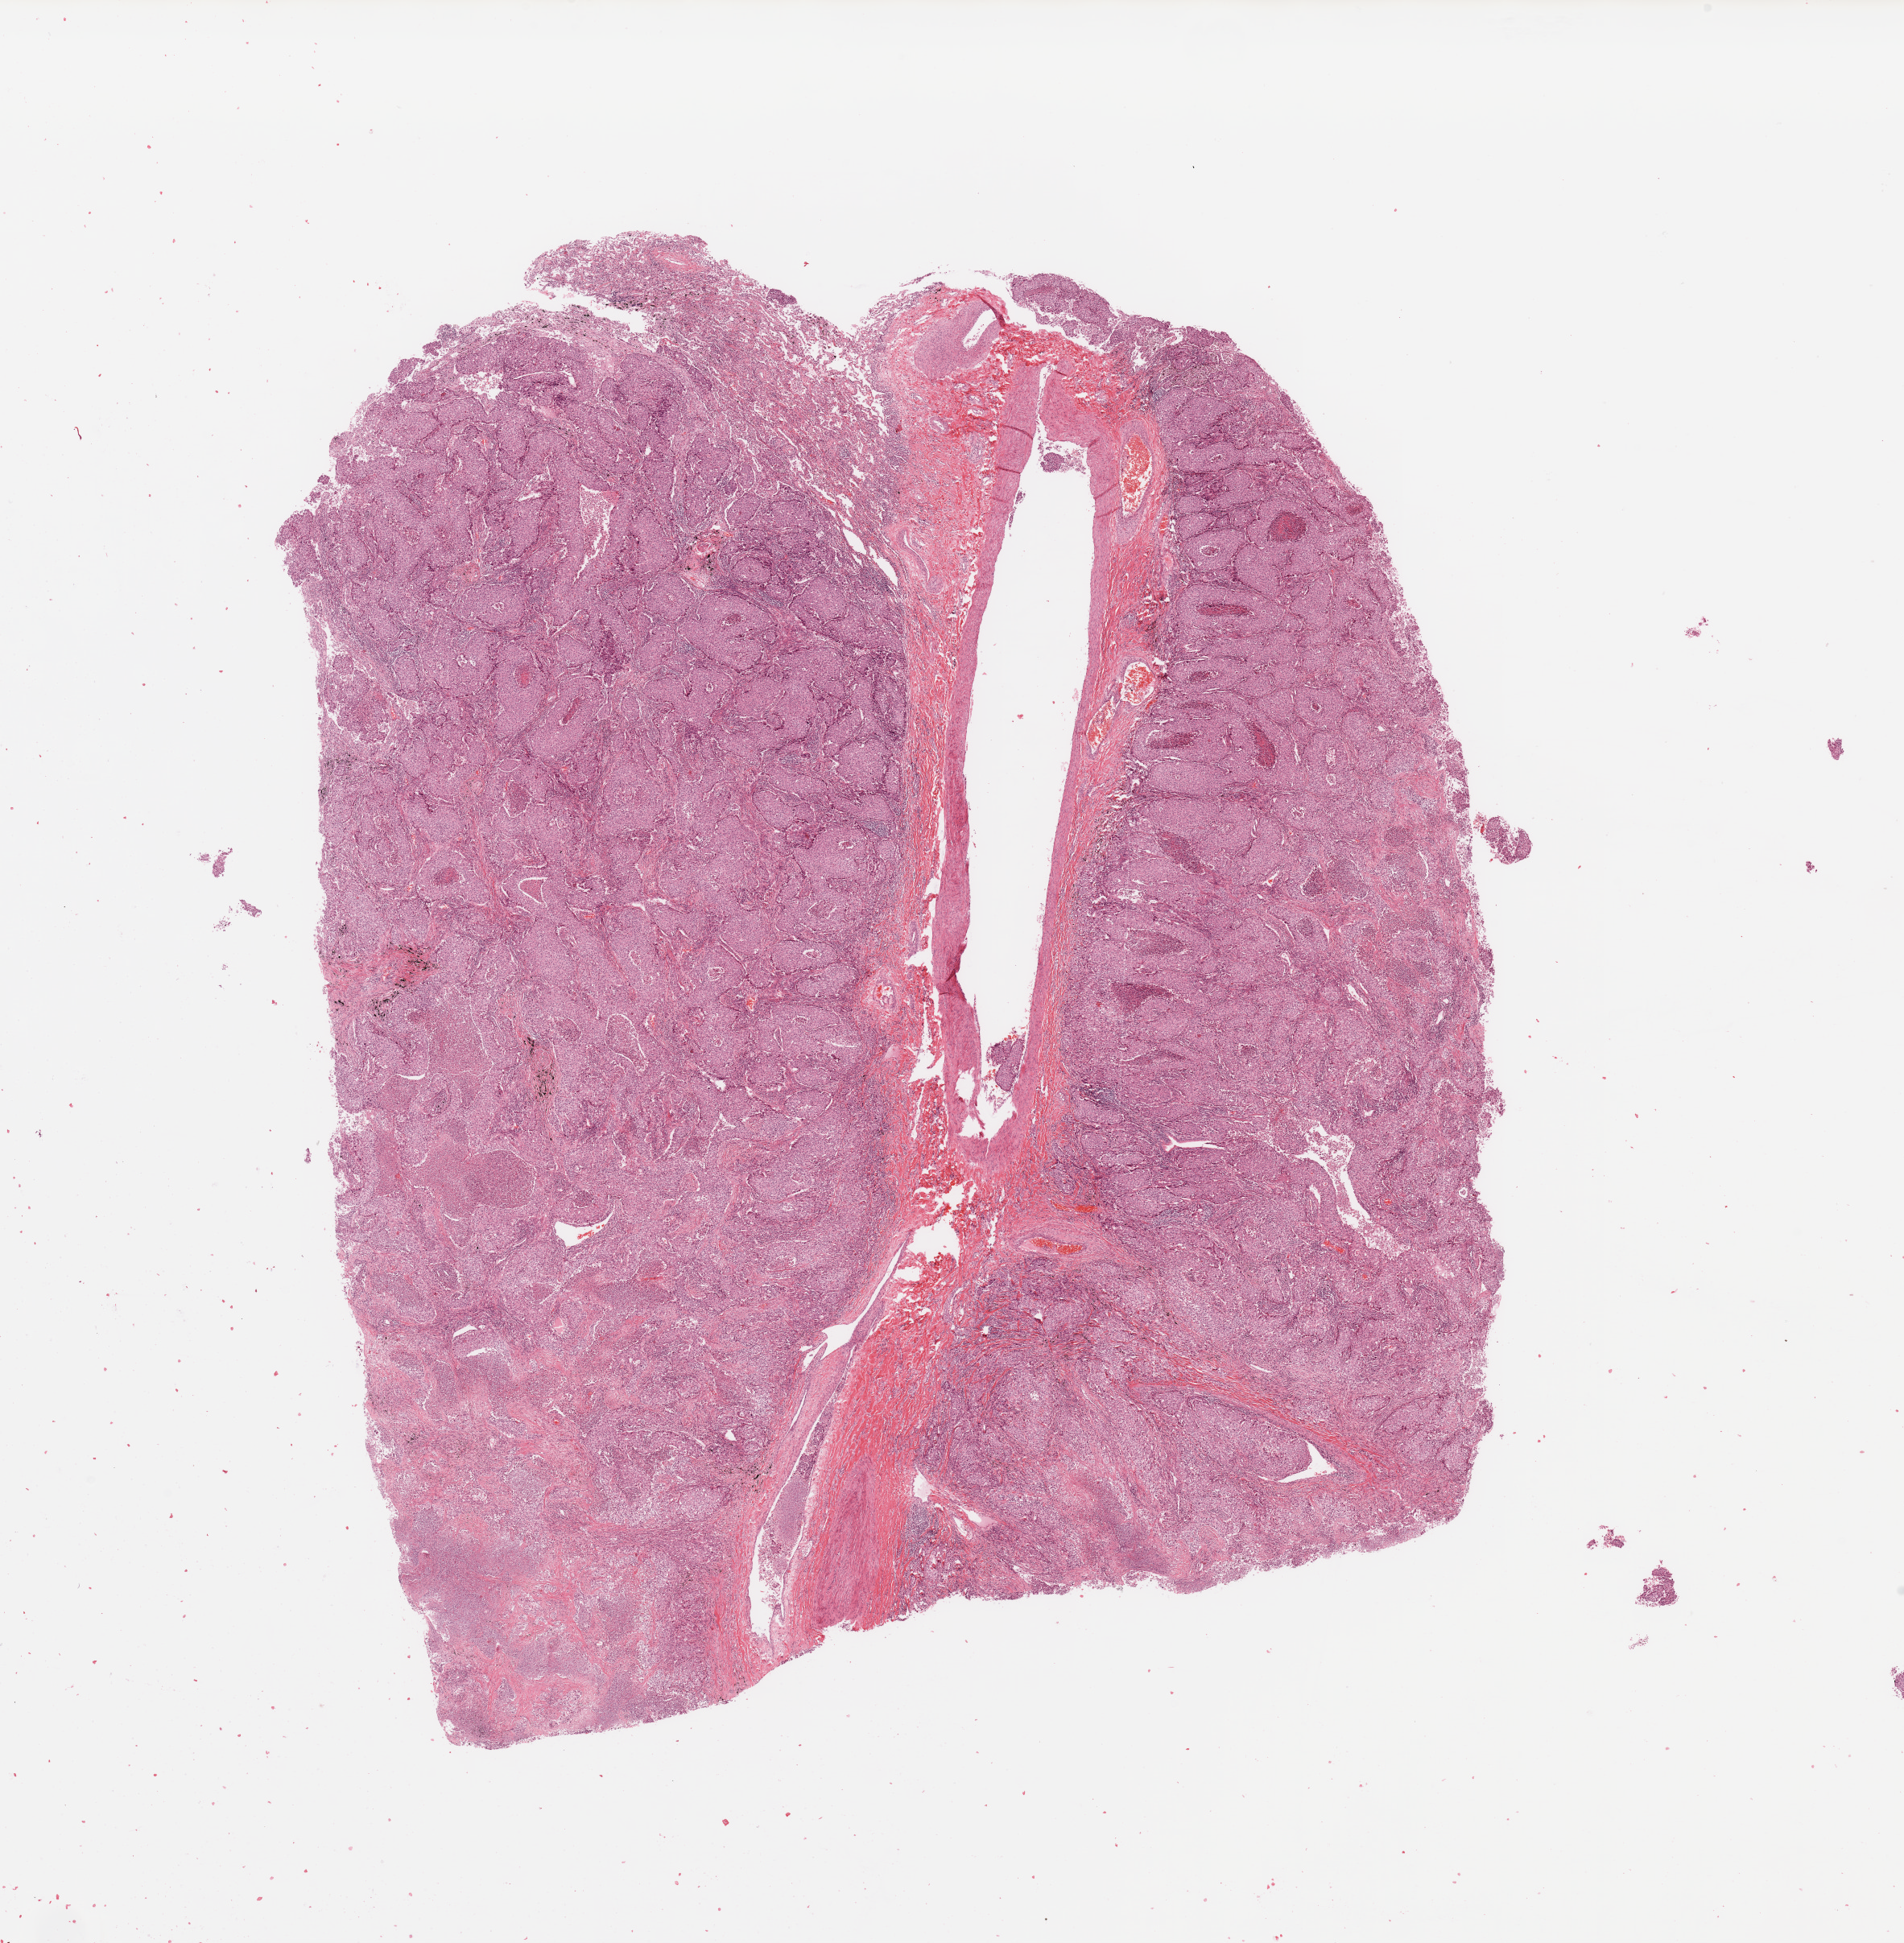
Digitized Hematoxylin and eosin (H&E) stained tissue section (whole slide) — shown as a low-resolution overview of the whole scanned area (about 18.7 x 19.1 mm, from a 20x scan); lung, tumour tissue. Patient: male, age 58 years. Histologic grade: G3 (poorly differentiated).
- diagnosis: Adenocarcinoma, NOS
- AJCC pathologic stage: IIA